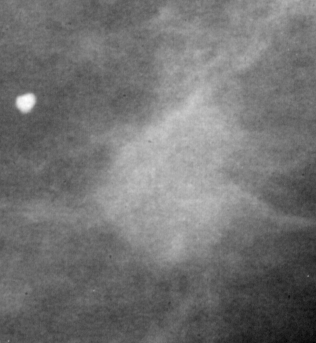
Crop from a digitized film mammogram around one marked abnormality; right breast; CC view; BI-RADS breast density category 3 (scale 1–4).
Finding: mass, shape lobulated, margins ill defined; BI-RADS assessment category 4; pathology result (as recorded, not read from the image): malignant.